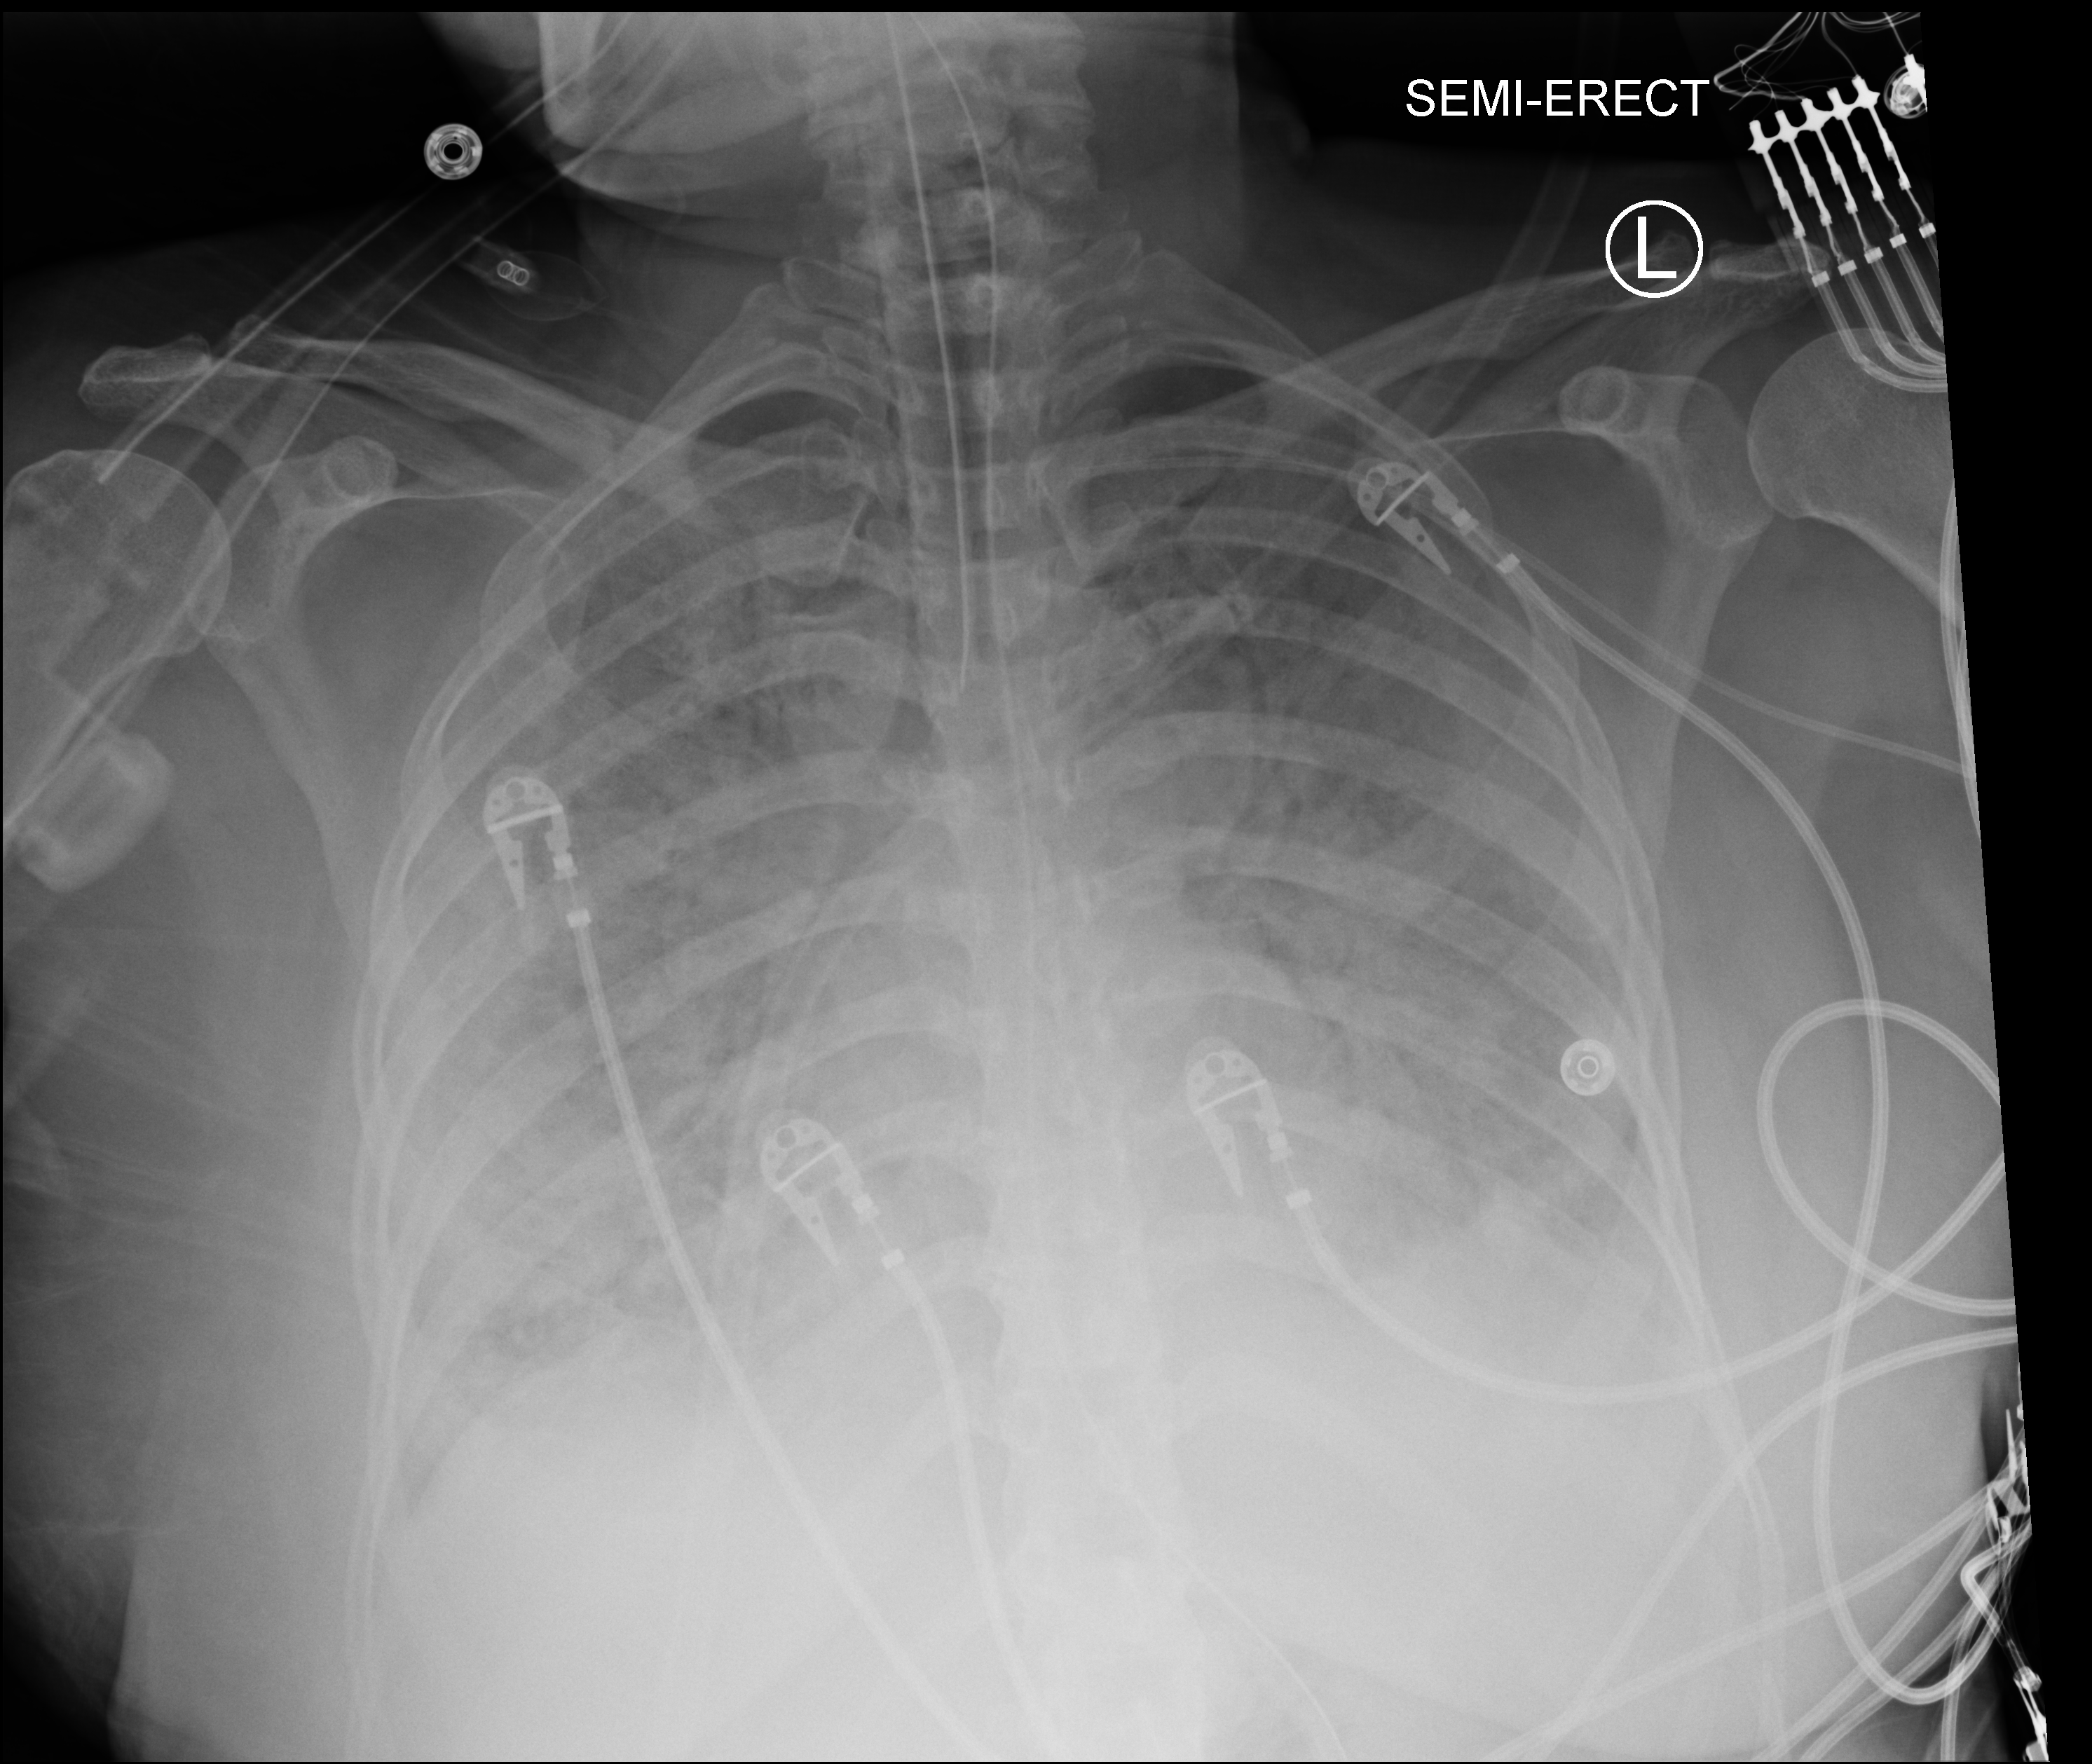
Portable chest radiograph, anteroposterior (AP) projection. Patient hospitalised with COVID-19; male, aged 18–59 years.
Admission-level facts for this patient (not findings on this image; timing relative to this image not recorded):
- admitted to intensive care during this hospital stay: yes